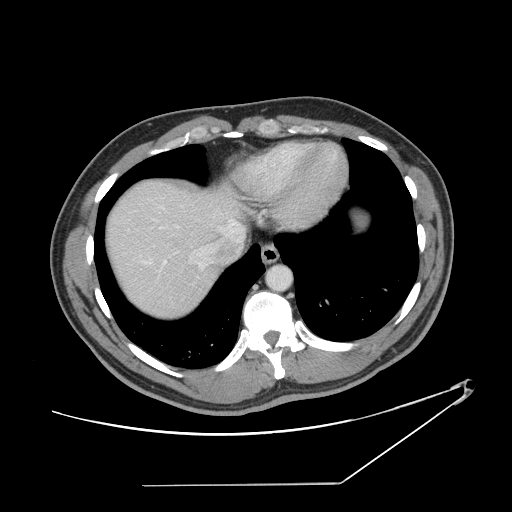
Contrast-enhanced abdominal CT, one axial slice; slice 129 of 152 in the series (ordered by position); reconstruction kernel STANDARD; 120 kVp; intravenous contrast given; soft-tissue window (W 400 / L 40 HU); 2.5 mm slice thickness; 512 × 512 image matrix. Male patient, age 45 years. Case-level facts recorded for this patient, not image findings: diagnosis: colorectal cancer liver metastases, imaged before liver resection; multiple liver metastases: no; largest metastasis: 1 cm; disease in both lobes: no.
Annotated regions visible in this slice (expert manual segmentation):
- hepatic veins: bounding box <128,207,242,269> (left, top, right, bottom; pixels)
- liver: <109,181,235,317>
- planned liver remnant (the part of the liver to remain after resection): <109,182,229,317>